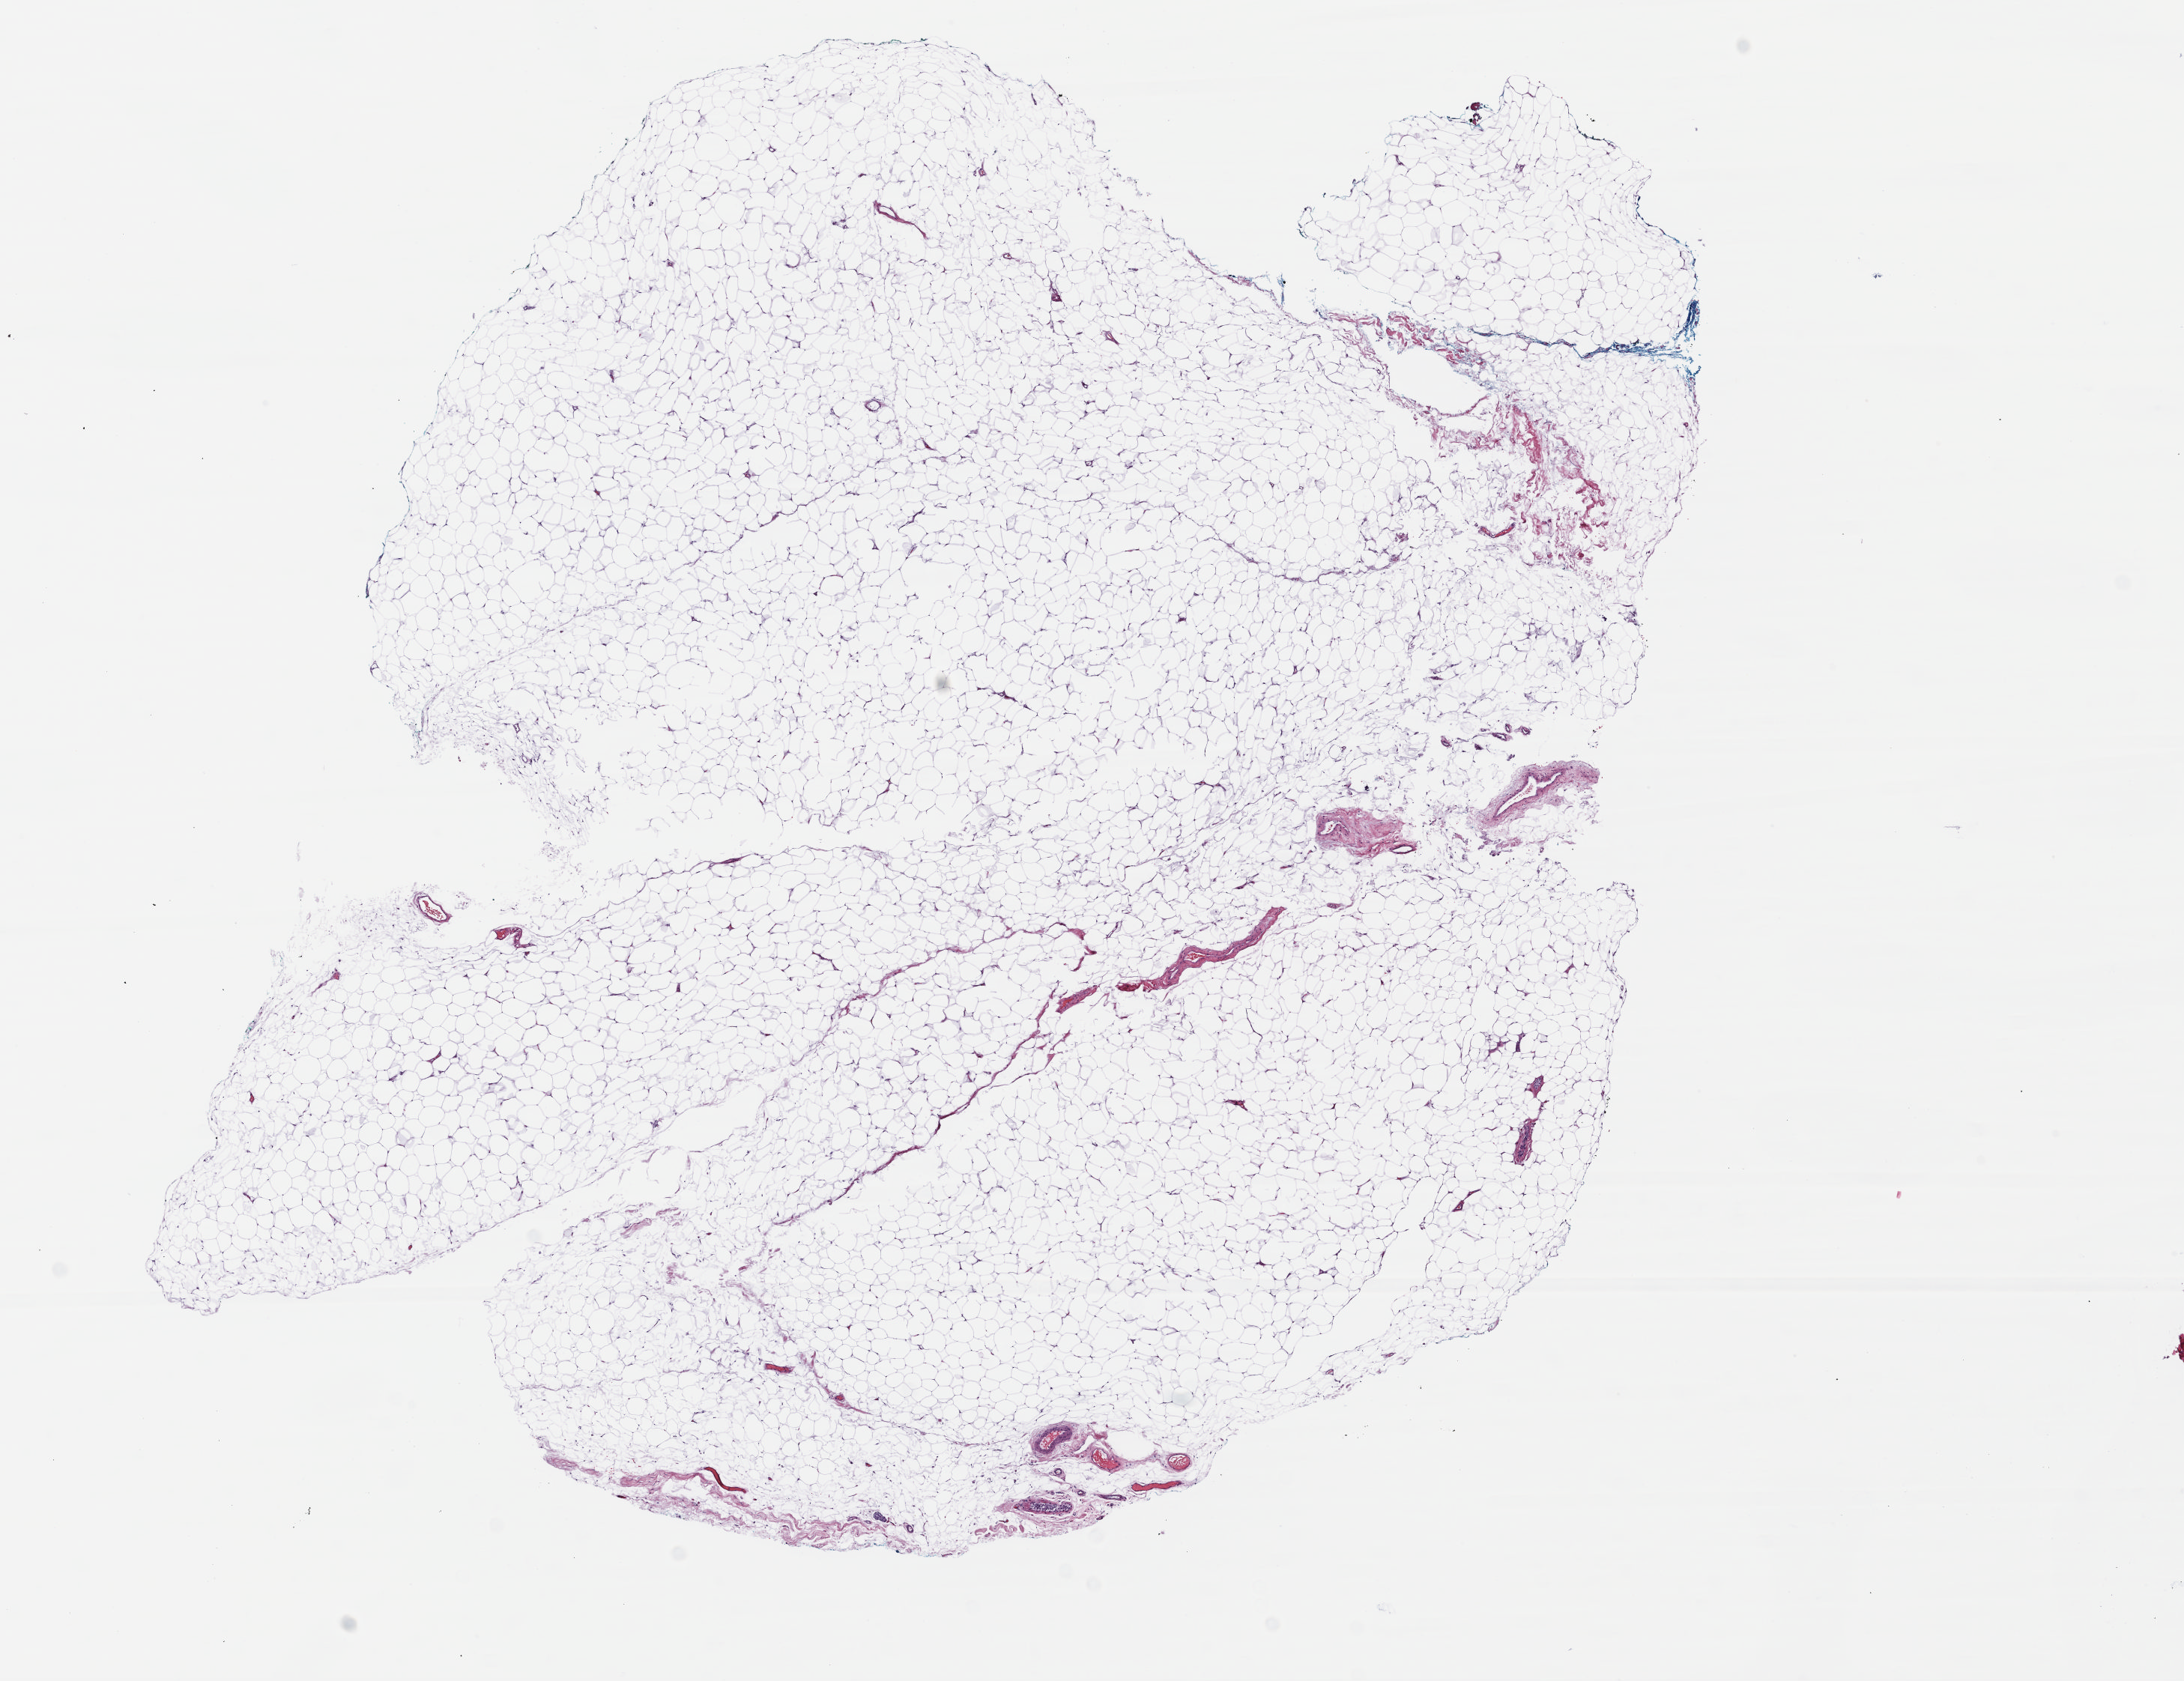
H&E whole-slide image, low-resolution overview of the scanned area, about 11.5 x 8.8 mm (acquisition: 40x scan); FFPE section; primary tumour sample from the breast. Female patient; age at initial diagnosis 68 years.
• lymph nodes positive (case pathology): 0 of 2 examined
• AJCC pathologic stage: IIA (7th edition)
• diagnosis: Infiltrating duct carcinoma, NOS